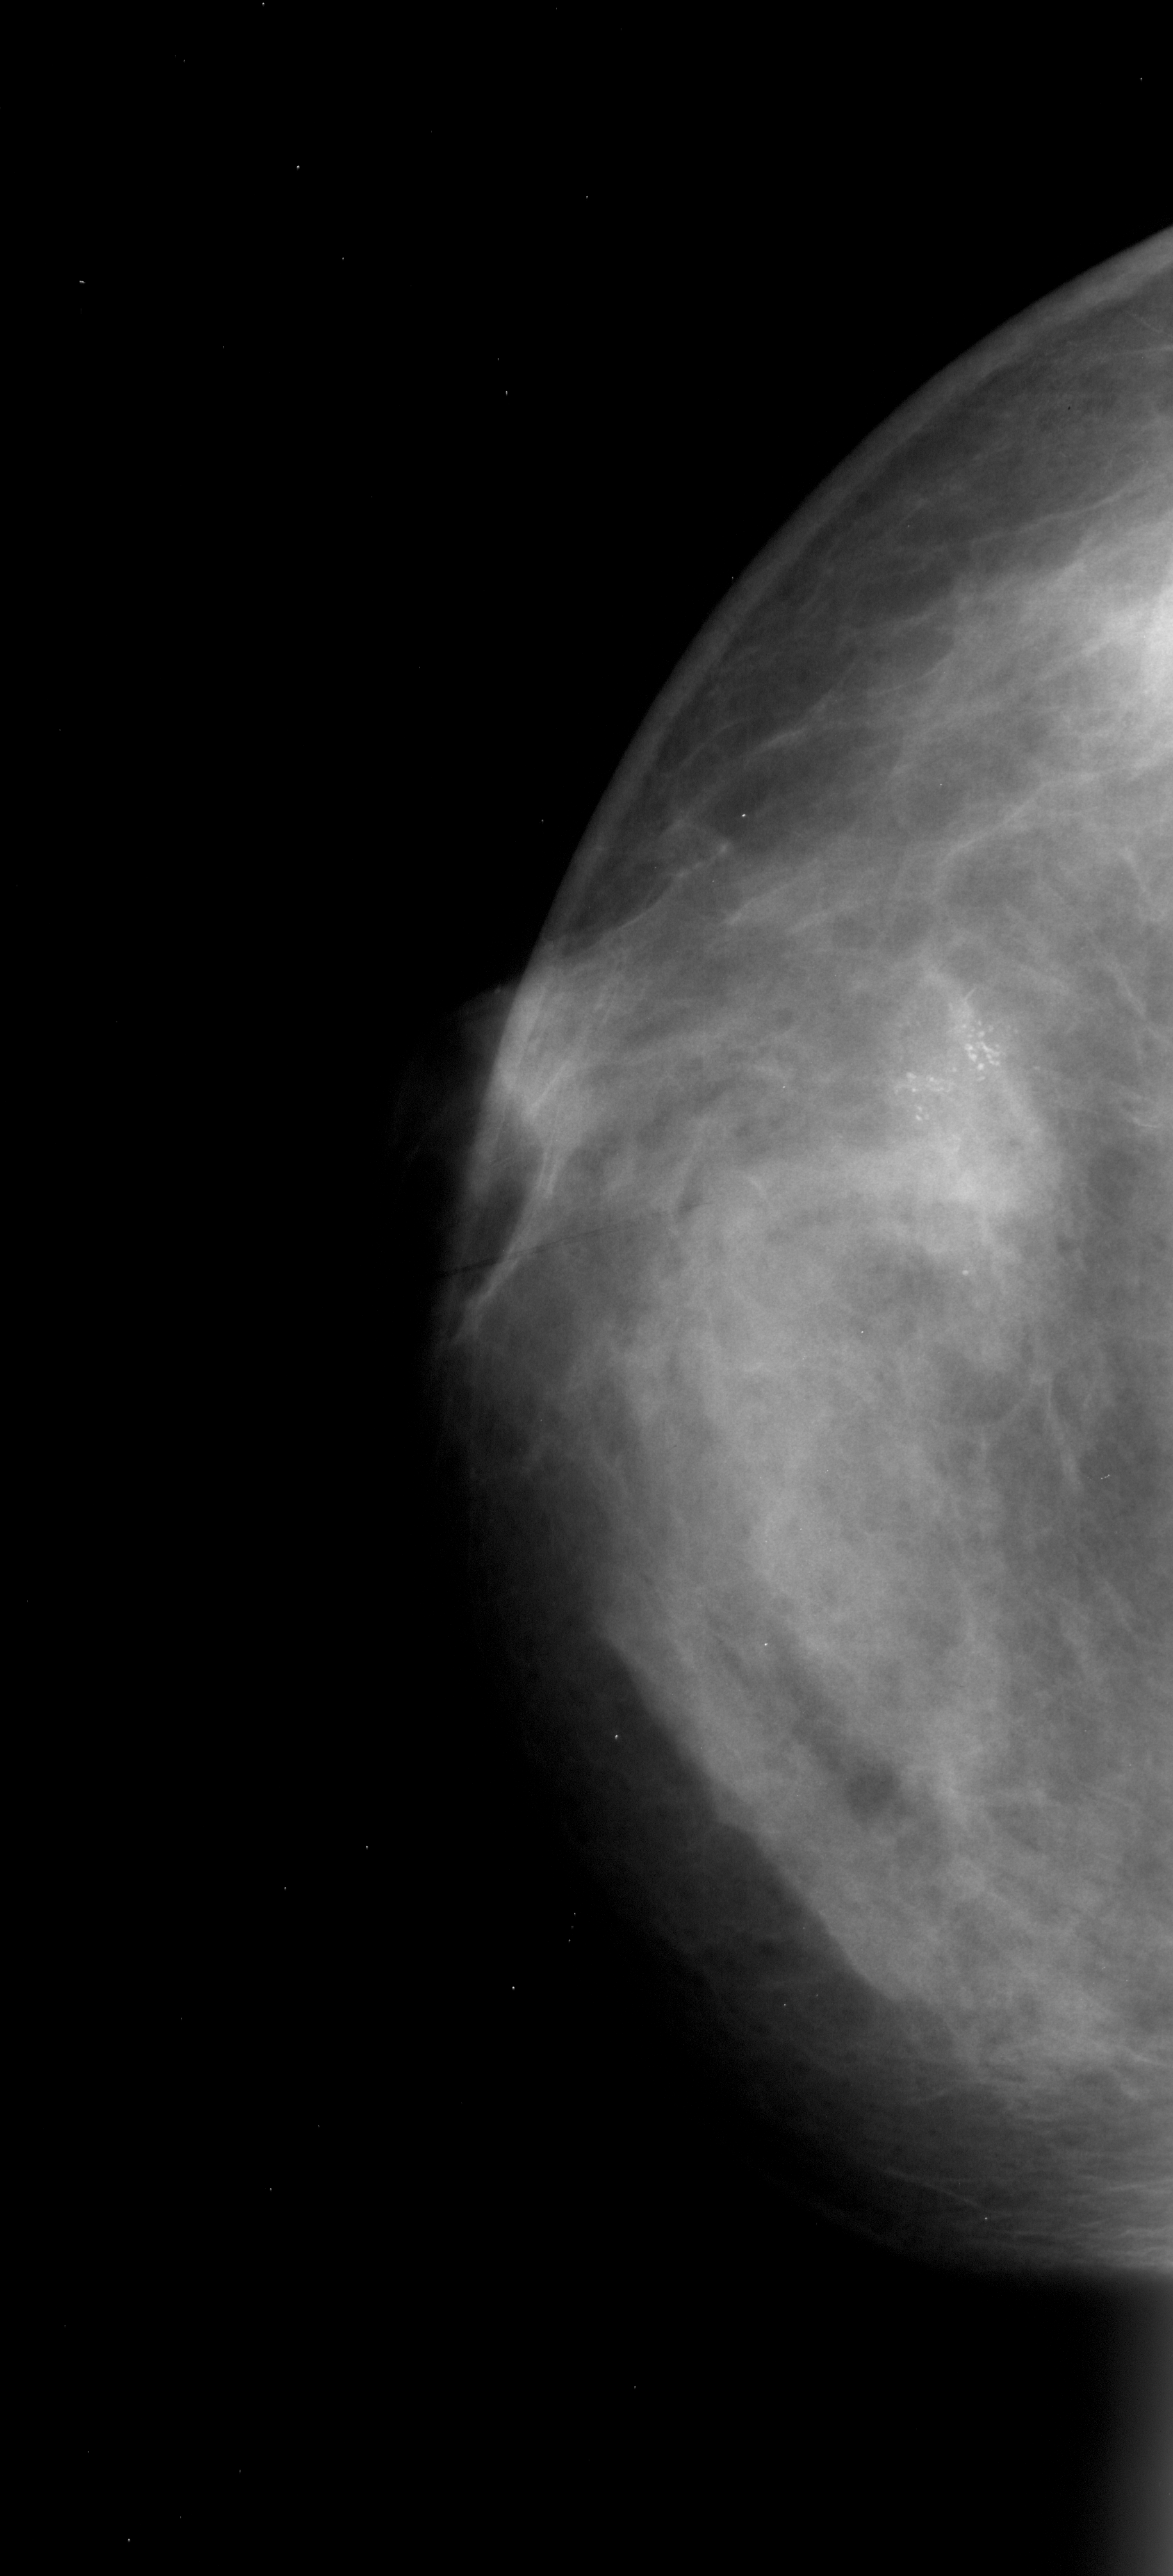
Scanned film-screen mammogram, left breast, CC view, BI-RADS breast density category 4 (scale 1–4).
- Marked abnormality: calcifications, morphology pleomorphic, distribution clustered; BI-RADS assessment category 4; subtlety rating 5 on a 1 (subtle) to 5 (obvious) scale; pathology (as recorded): malignant.